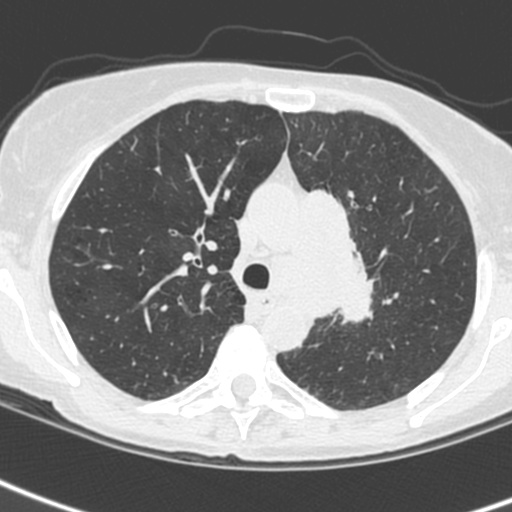
Low-dose screening chest CT, one axial slice. Slice 171 of 242 in the series (ordered by position). 120 kVp. Lung window (W 1500 / L -600 HU). 1.3 mm slice thickness. 512 × 512 image matrix, field of view 284 × 284 mm.
Outlined on this slice (outlined manually by an expert reader):
- lesion 3 (tumor, upper lobe of left lung): bounding box [x1, y1, x2, y2] px = [309, 190, 374, 323]